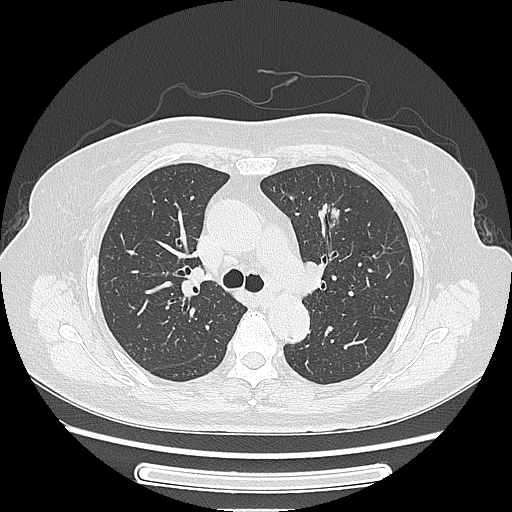
Chest CT, one axial slice. Slice 160 of 227 in the series (ordered by position). 120 kVp. Lung window (W 1500 / L -600 HU). 512 × 512 image matrix, field of view 363 × 363 mm. Patient: female, 77 years. From the clinical record (not read from this slice): clinical TNM (as recorded): T1c N3 M0.
Outlined on this slice (bounding box drawn by a radiologist):
- lung tumour (recorded histology: adenocarcinoma): bounding box (x1, y1, x2, y2) in pixels: (311, 192, 345, 244)